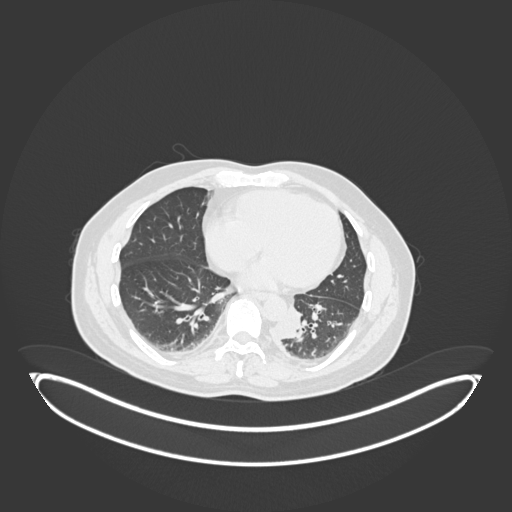
Chest CT, one axial slice. Slice 63 of 258 in the series (ordered by position). 120 kVp. Lung window (W 1500 / L -600 HU). 1 mm slice thickness. 512 × 512 image matrix, field of view 500 × 500 mm. Male patient, age 54 years. From the clinical record (not read from this slice): clinical TNM (as recorded): T3 N0 M0.
Structures marked on this image (bounding box drawn by a radiologist):
- lung tumour (recorded histology: squamous cell carcinoma): box from (x=276, y=309) to (x=308, y=342) px